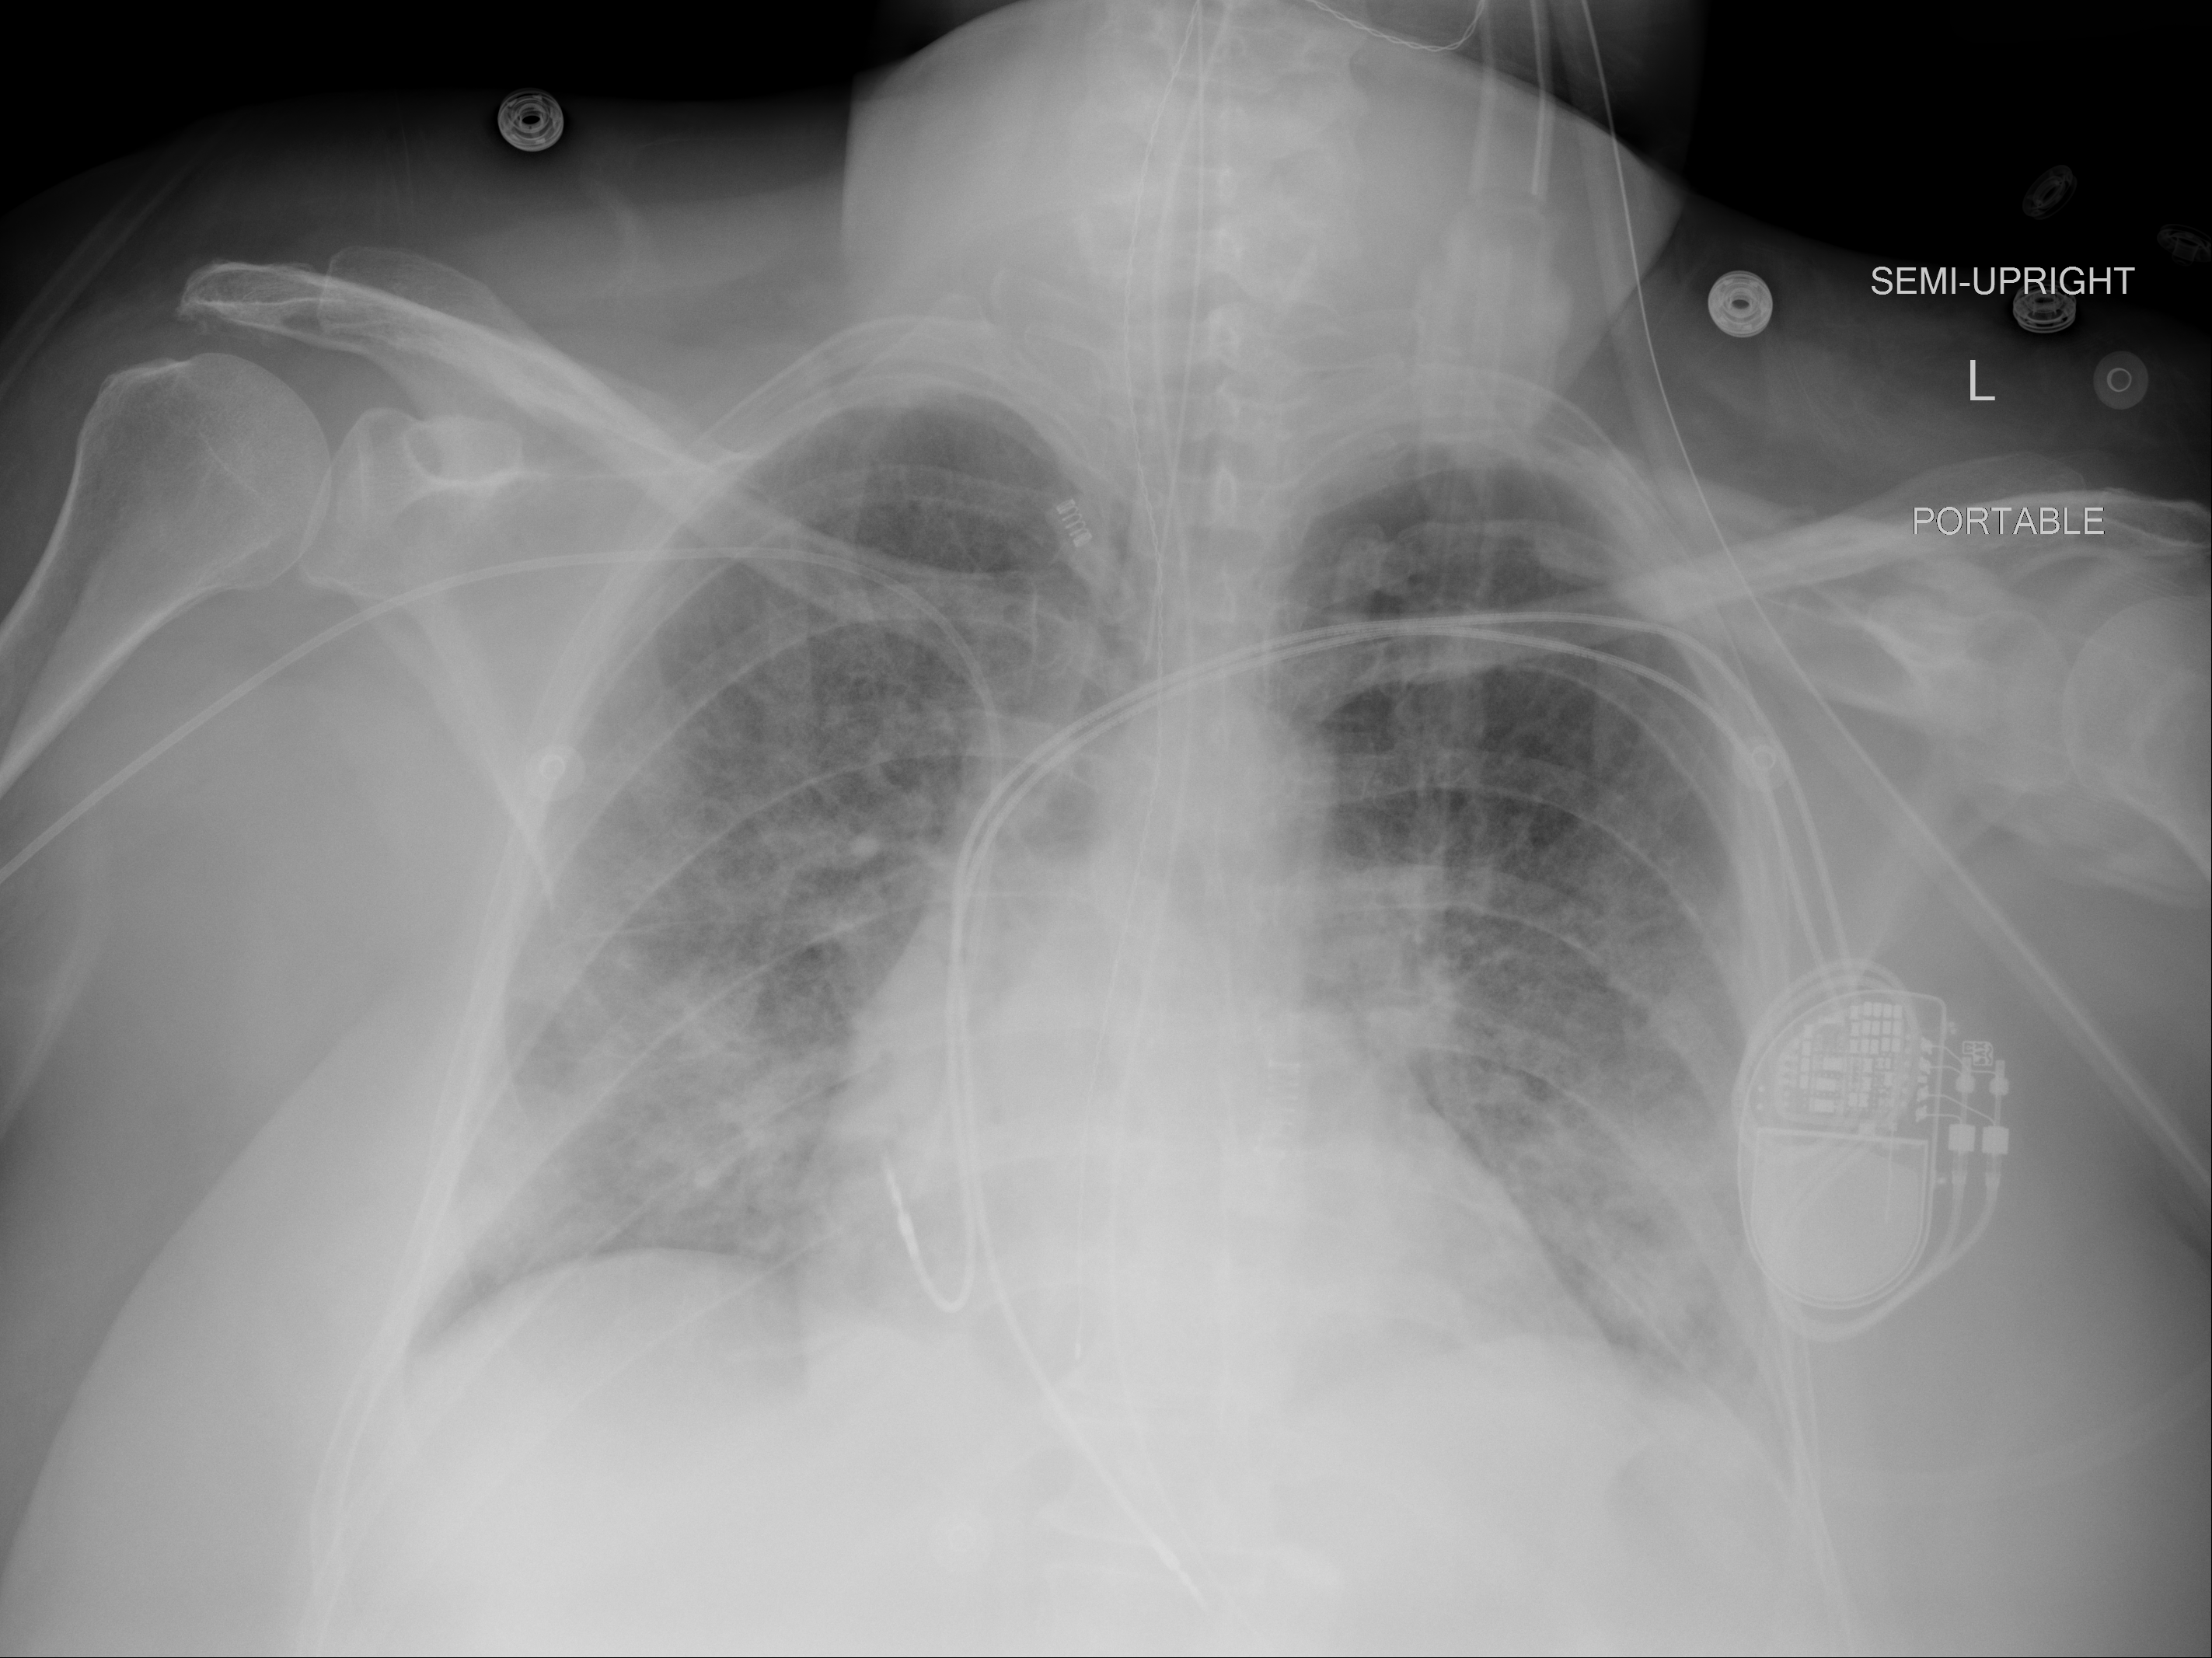
Chest X-ray (portable), AP projection. Female patient, age 57 years; imaged 4 days after the COVID-19 diagnosis.
Key findings recorded by the radiologist: no significant change in bilateral airspace opacities and interstitial prominence from the prior study.